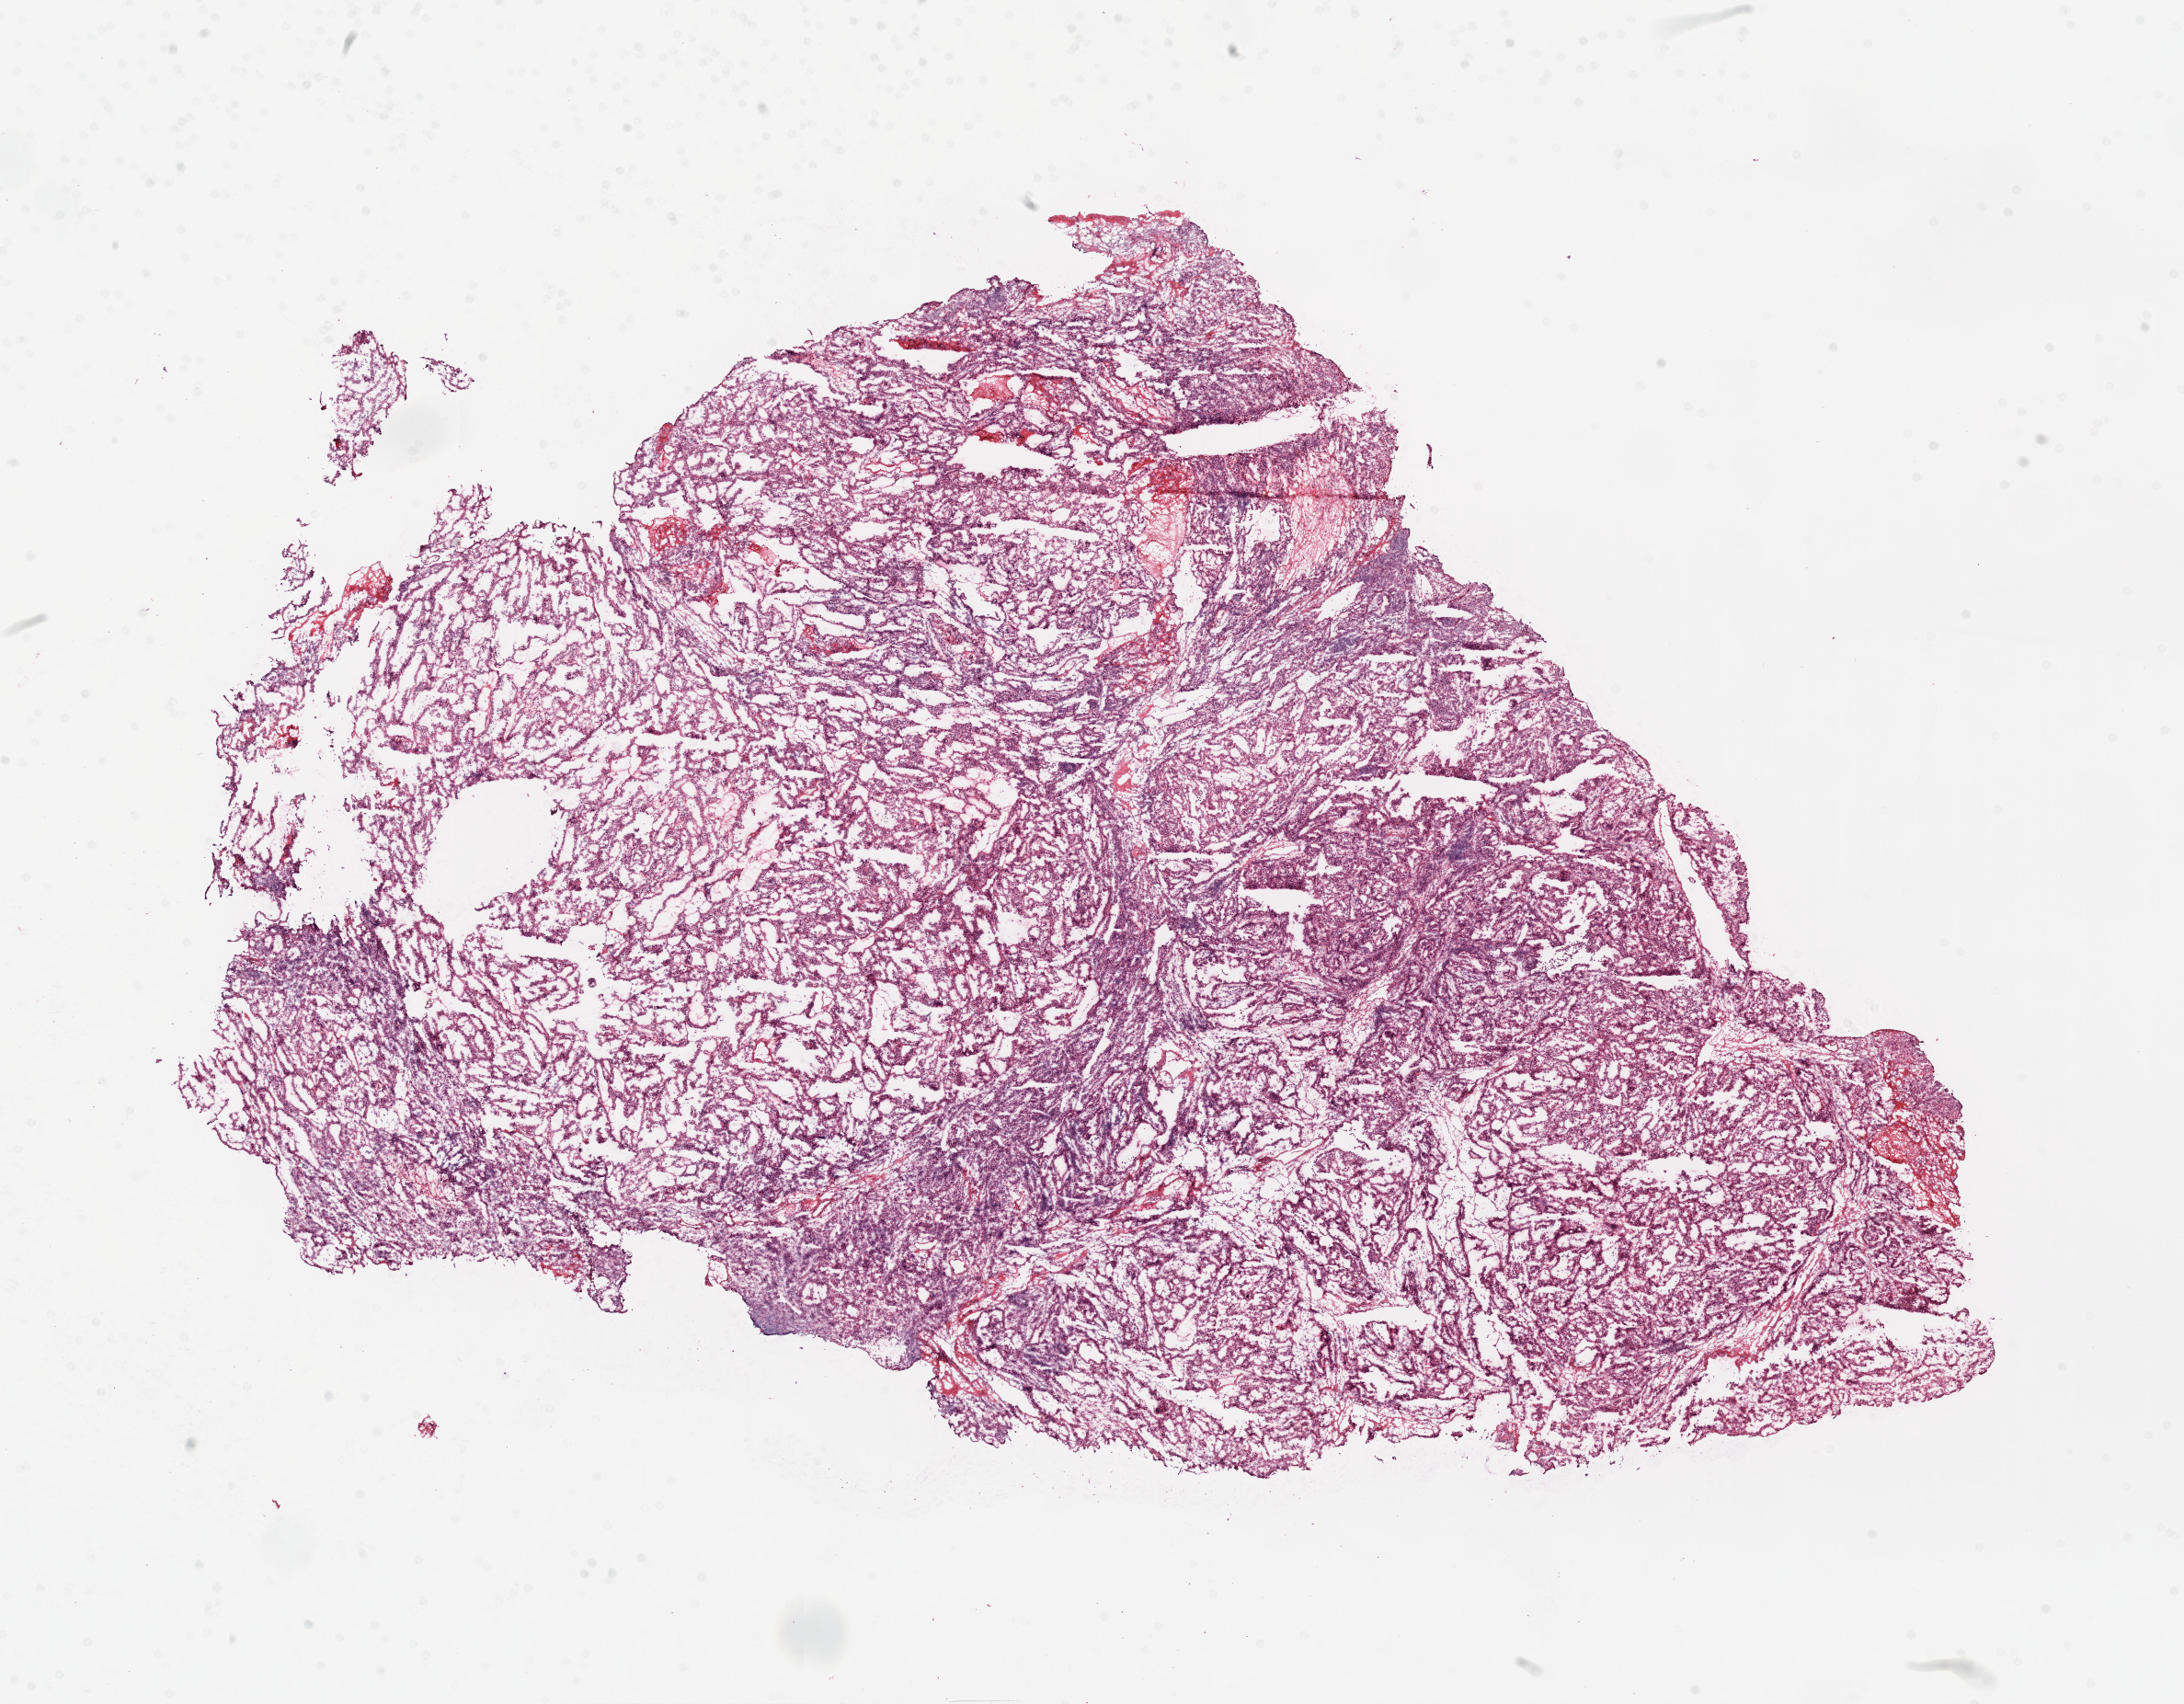
Whole-slide histology image, H&E — shown as a low-resolution overview of the whole scanned area (about 19.1 x 14.9 mm, acquisition: 20x scan). Frozen section from the top of the tissue portion. Primary tumour sample from the kidney. Male, age 46 years at initial diagnosis. Histologic grade: G2 (moderately differentiated). Pathologist review of this section (percent, as recorded): tumour cells 90%, tumour nuclei 80%, normal cells 0%, stromal cells 10%, necrosis 0%.
AJCC pathologic stage: I. Diagnosis: Clear cell adenocarcinoma, NOS.